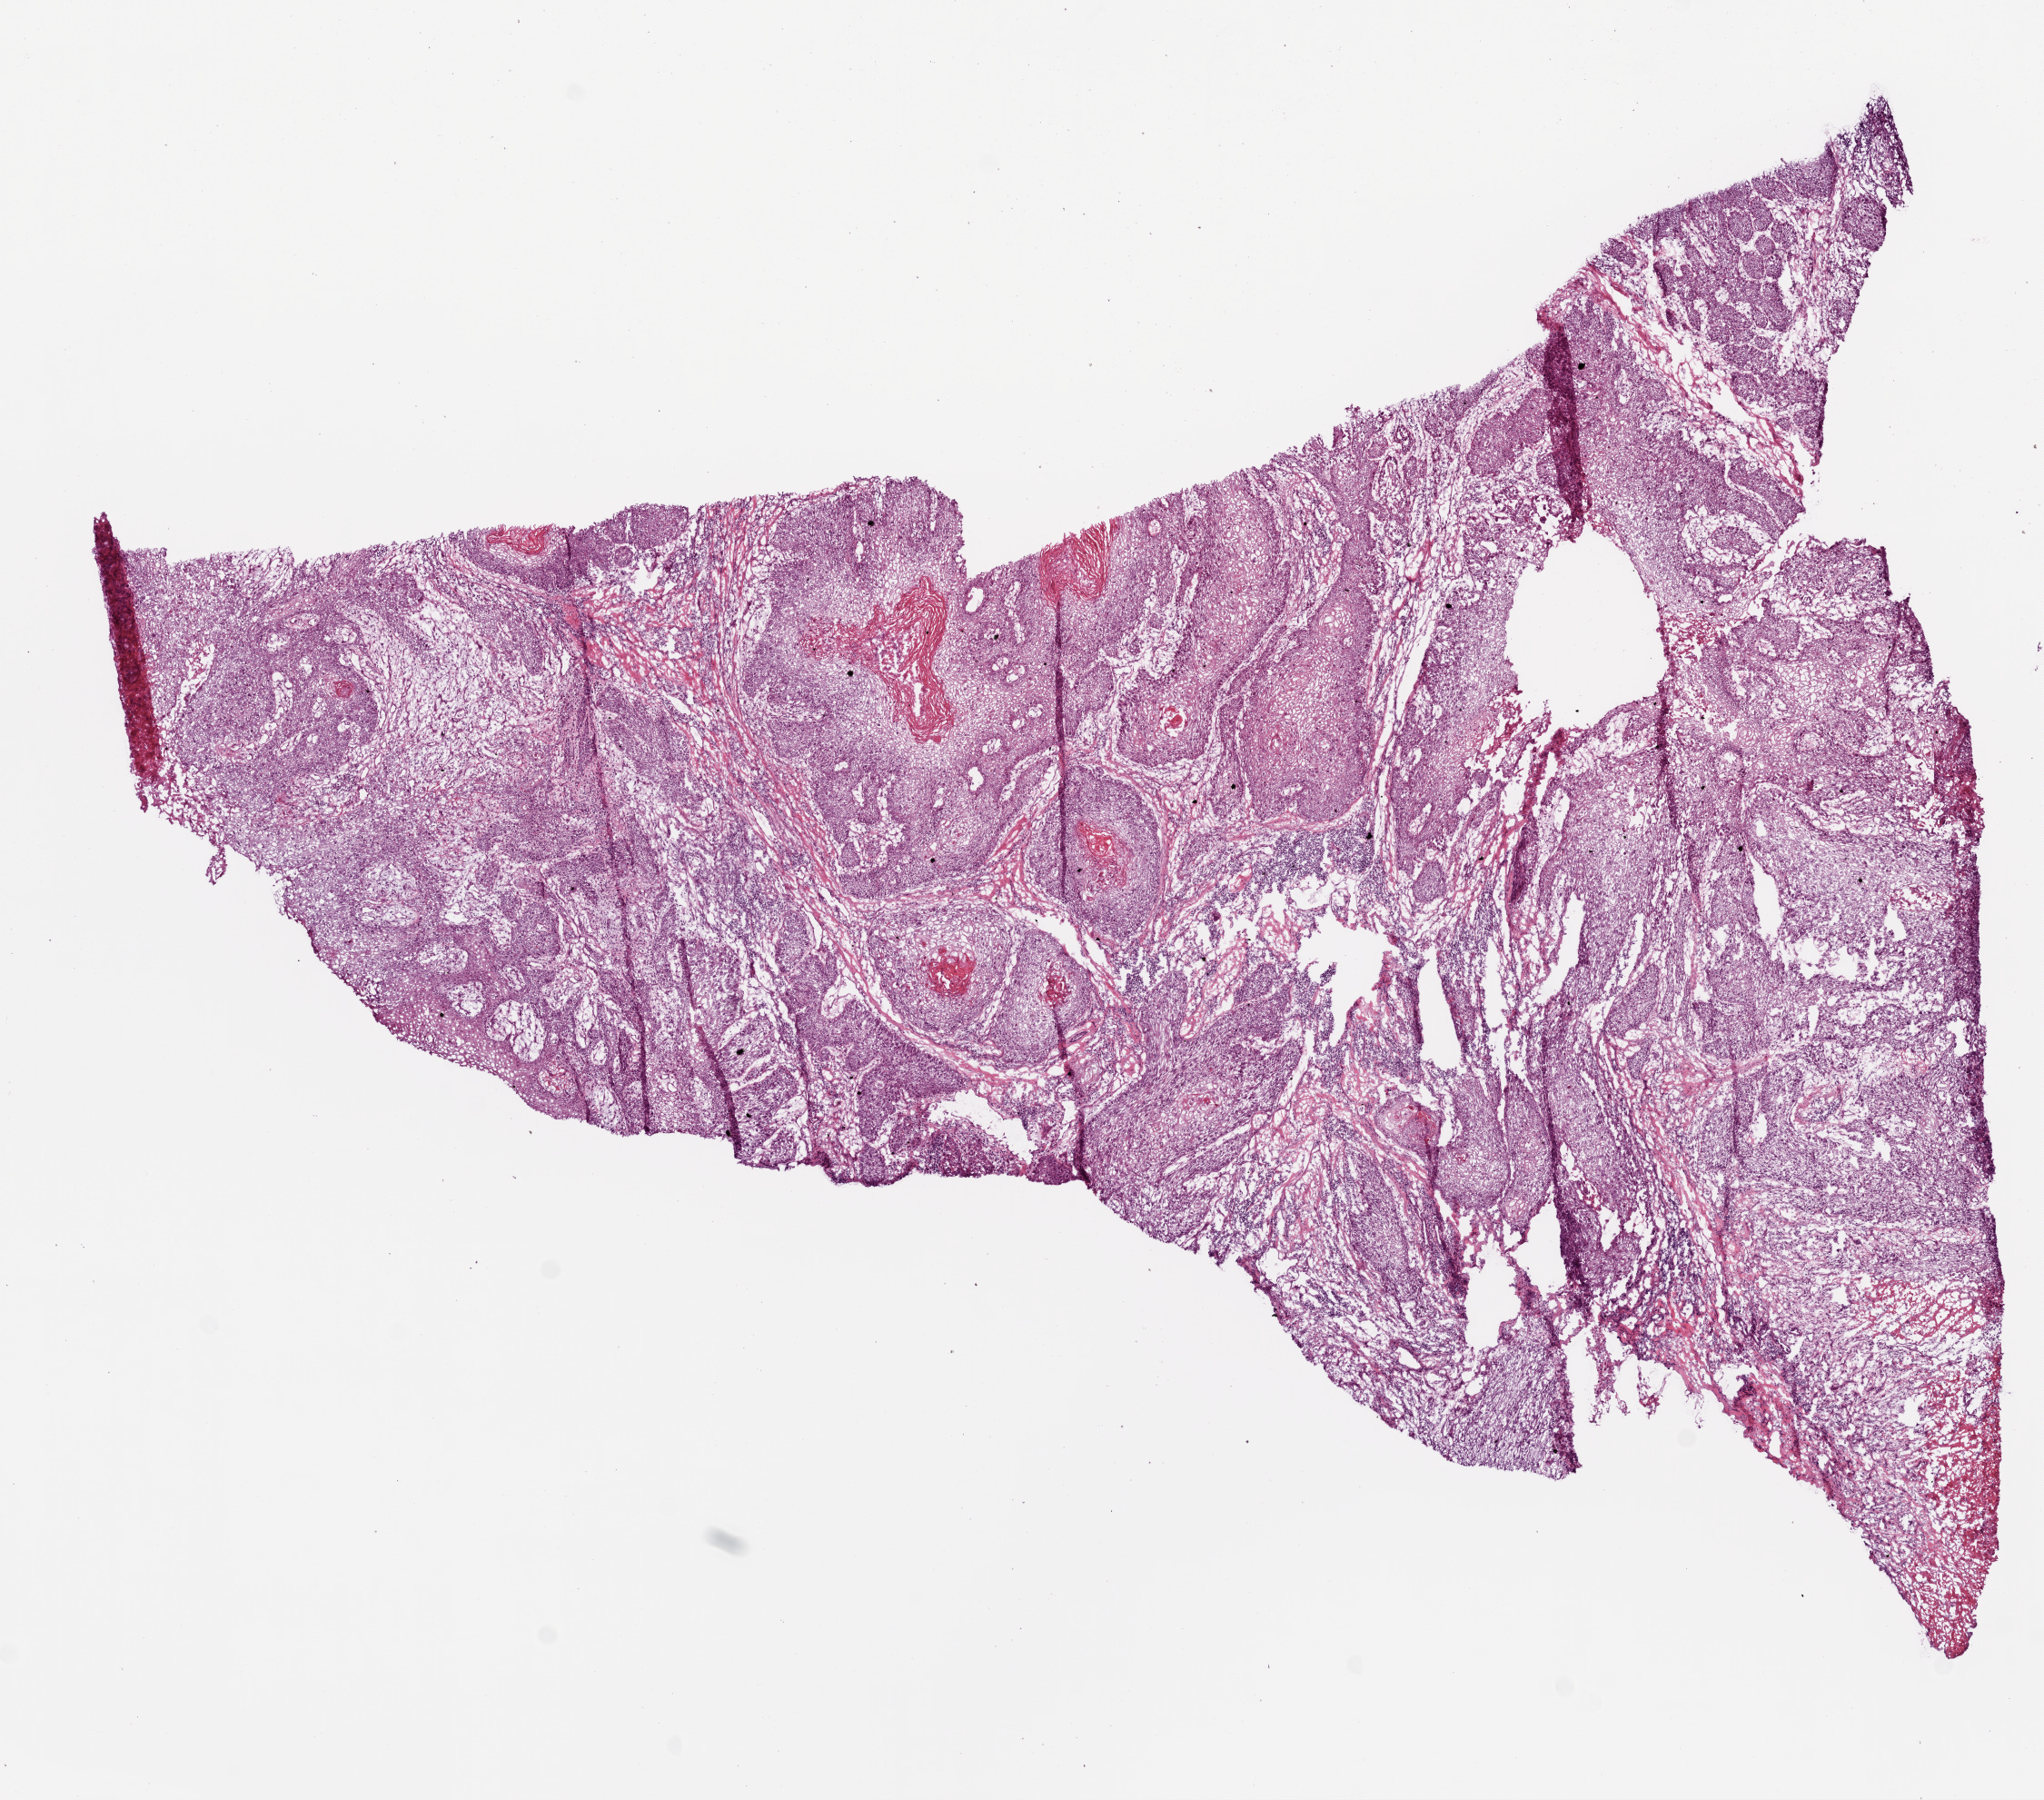
Hematoxylin and eosin (H&E) stained whole-slide image, shown as a low-resolution overview of the whole scanned area (about 9.0 x 7.9 mm, from a 20x scan), frozen section from the bottom of the tissue portion, sample: primary tumour, head and neck. Patient: male, age at initial diagnosis 56 years. Histologic grade: G2 (moderately differentiated). Slide review estimates, as recorded: tumour cells 80%, tumour nuclei 85%, normal cells 10%, stromal cells 15%, necrosis 0%.
- diagnosis: Squamous cell carcinoma, NOS (larynx, NOS)
- AJCC pathologic stage: III (7th edition)